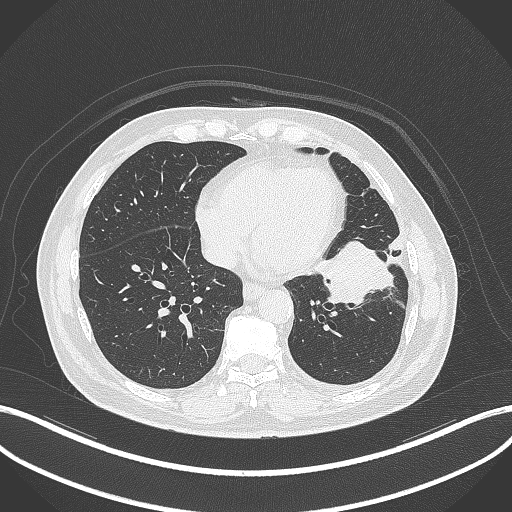
Chest CT, one axial slice. Slice 123 of 230 in the series (ordered by position). Reconstruction kernel B70f. 120 kVp. Lung window (W 1500 / L -600 HU). 1 mm slice thickness. 512 × 512 image matrix. Male patient, age 68 years. From the clinical record (not read from this slice): clinical TNM (as recorded): T2b N0 M0.
Annotated regions visible in this slice (rectangle marked by the reading radiologist):
- lung tumour (recorded histology: squamous cell carcinoma): bounding box [x1, y1, x2, y2] px = [316, 237, 399, 311]